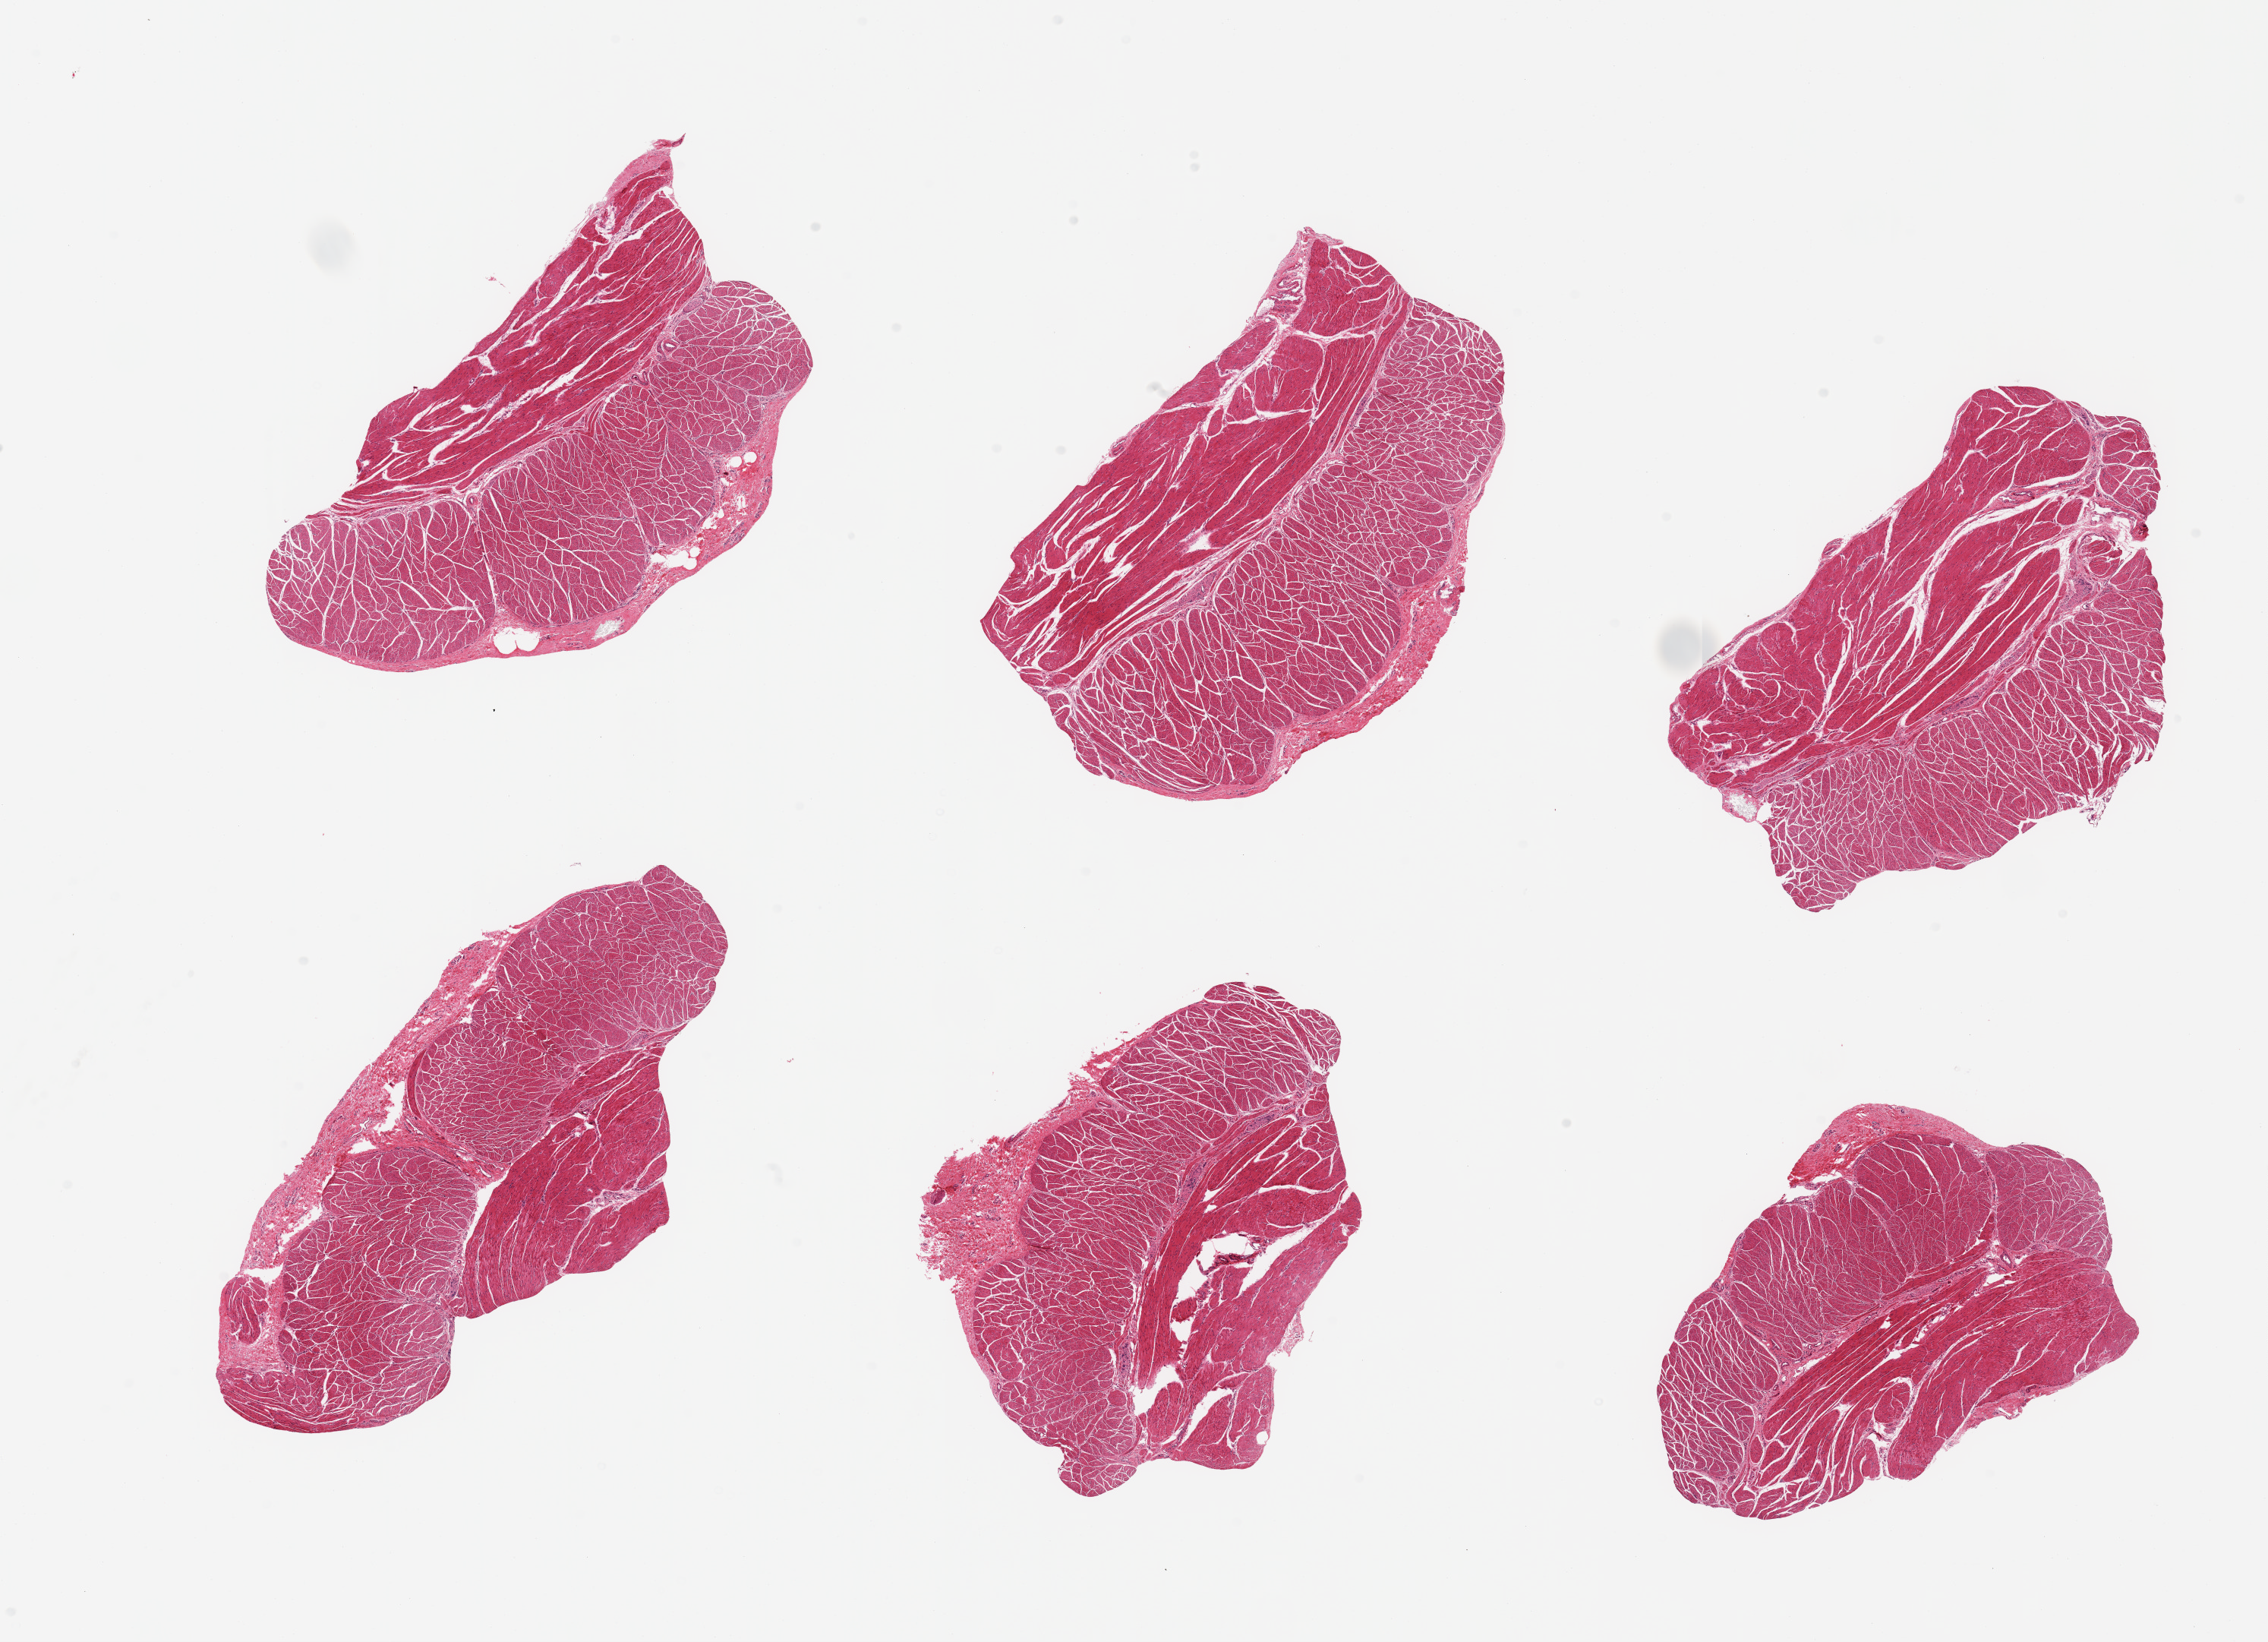
Digitized haematoxylin and eosin-stained section, shown as a low-resolution overview of the whole scanned area (about 23.6 x 17.1 mm, from a 20x scan), PAXgene-fixed paraffin-embedded (PFPE) section, sampled site (target tissue): esophageal muscle, donor tissue sample.
- pathologist's review note for this sample: 6 pieces, confirmed target muscularis